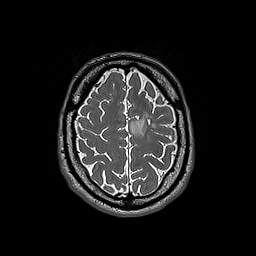
Brain MRI from a brain-tumour surgery series, one axial slice. Position 51 of 192 along the scan axis. 256 × 256 image matrix, field of view 250 × 250 mm. Case-level facts recorded for this patient, not image findings: histopathology: Oligodendroglioma; WHO grade: 3; IDH mutation: yes; tumour location: Left Frontal.
Structures marked on this image (outlined manually by an expert reader):
- tumour: bounding box <130,112,155,137> (left, top, right, bottom; pixels)